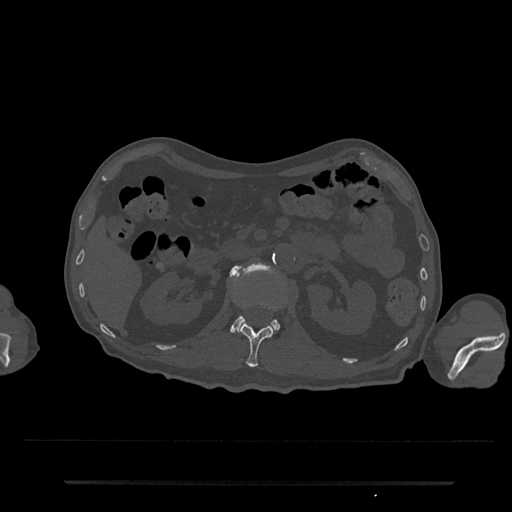
CT including the spine, one axial slice. Position 104 of 797 along the scan axis. 120 kVp. Bone window (W 1800 / L 400 HU). 0.5 mm slice thickness. 512 × 512 image matrix, field of view 427 × 427 mm. Male patient, age 74 years. From the clinical record (not read from this slice): primary cancer: prostate.
Outlined on this slice (semi-automatically segmented with operator editing):
- L1 vertebra: bounding box (x1, y1, x2, y2) in pixels: (240, 300, 284, 368)
- L2 vertebra: (230, 265, 279, 332)